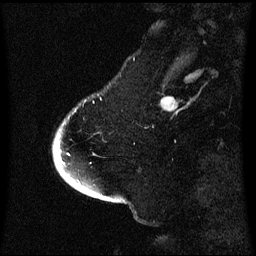
Breast MRI (dynamic contrast-enhanced), one sagittal slice; position 12 of 60 along the scan axis; dynamic contrast-enhanced series, image 2 of 3 at this slice position (ordered by acquisition); 1.5 T; TE 4.2 ms, TR 8.4 ms; 256 × 256 image matrix. Patient: female, 53 years. Case-level facts recorded for this patient, not image findings: setting: breast cancer imaged before/during neoadjuvant chemotherapy; receptor status: HR-positive, HER2-negative.
Structures marked on this image (semi-automatically segmented with operator editing):
- analysis volume of interest (the breast-tissue region the enhancement analysis was run in; not a lesion): bounding box <54,116,71,171> (left, top, right, bottom; pixels)
- tumour enhancement mask (voxels above the 70 % enhancement threshold inside the analysis volume of interest): <58,150,61,159>